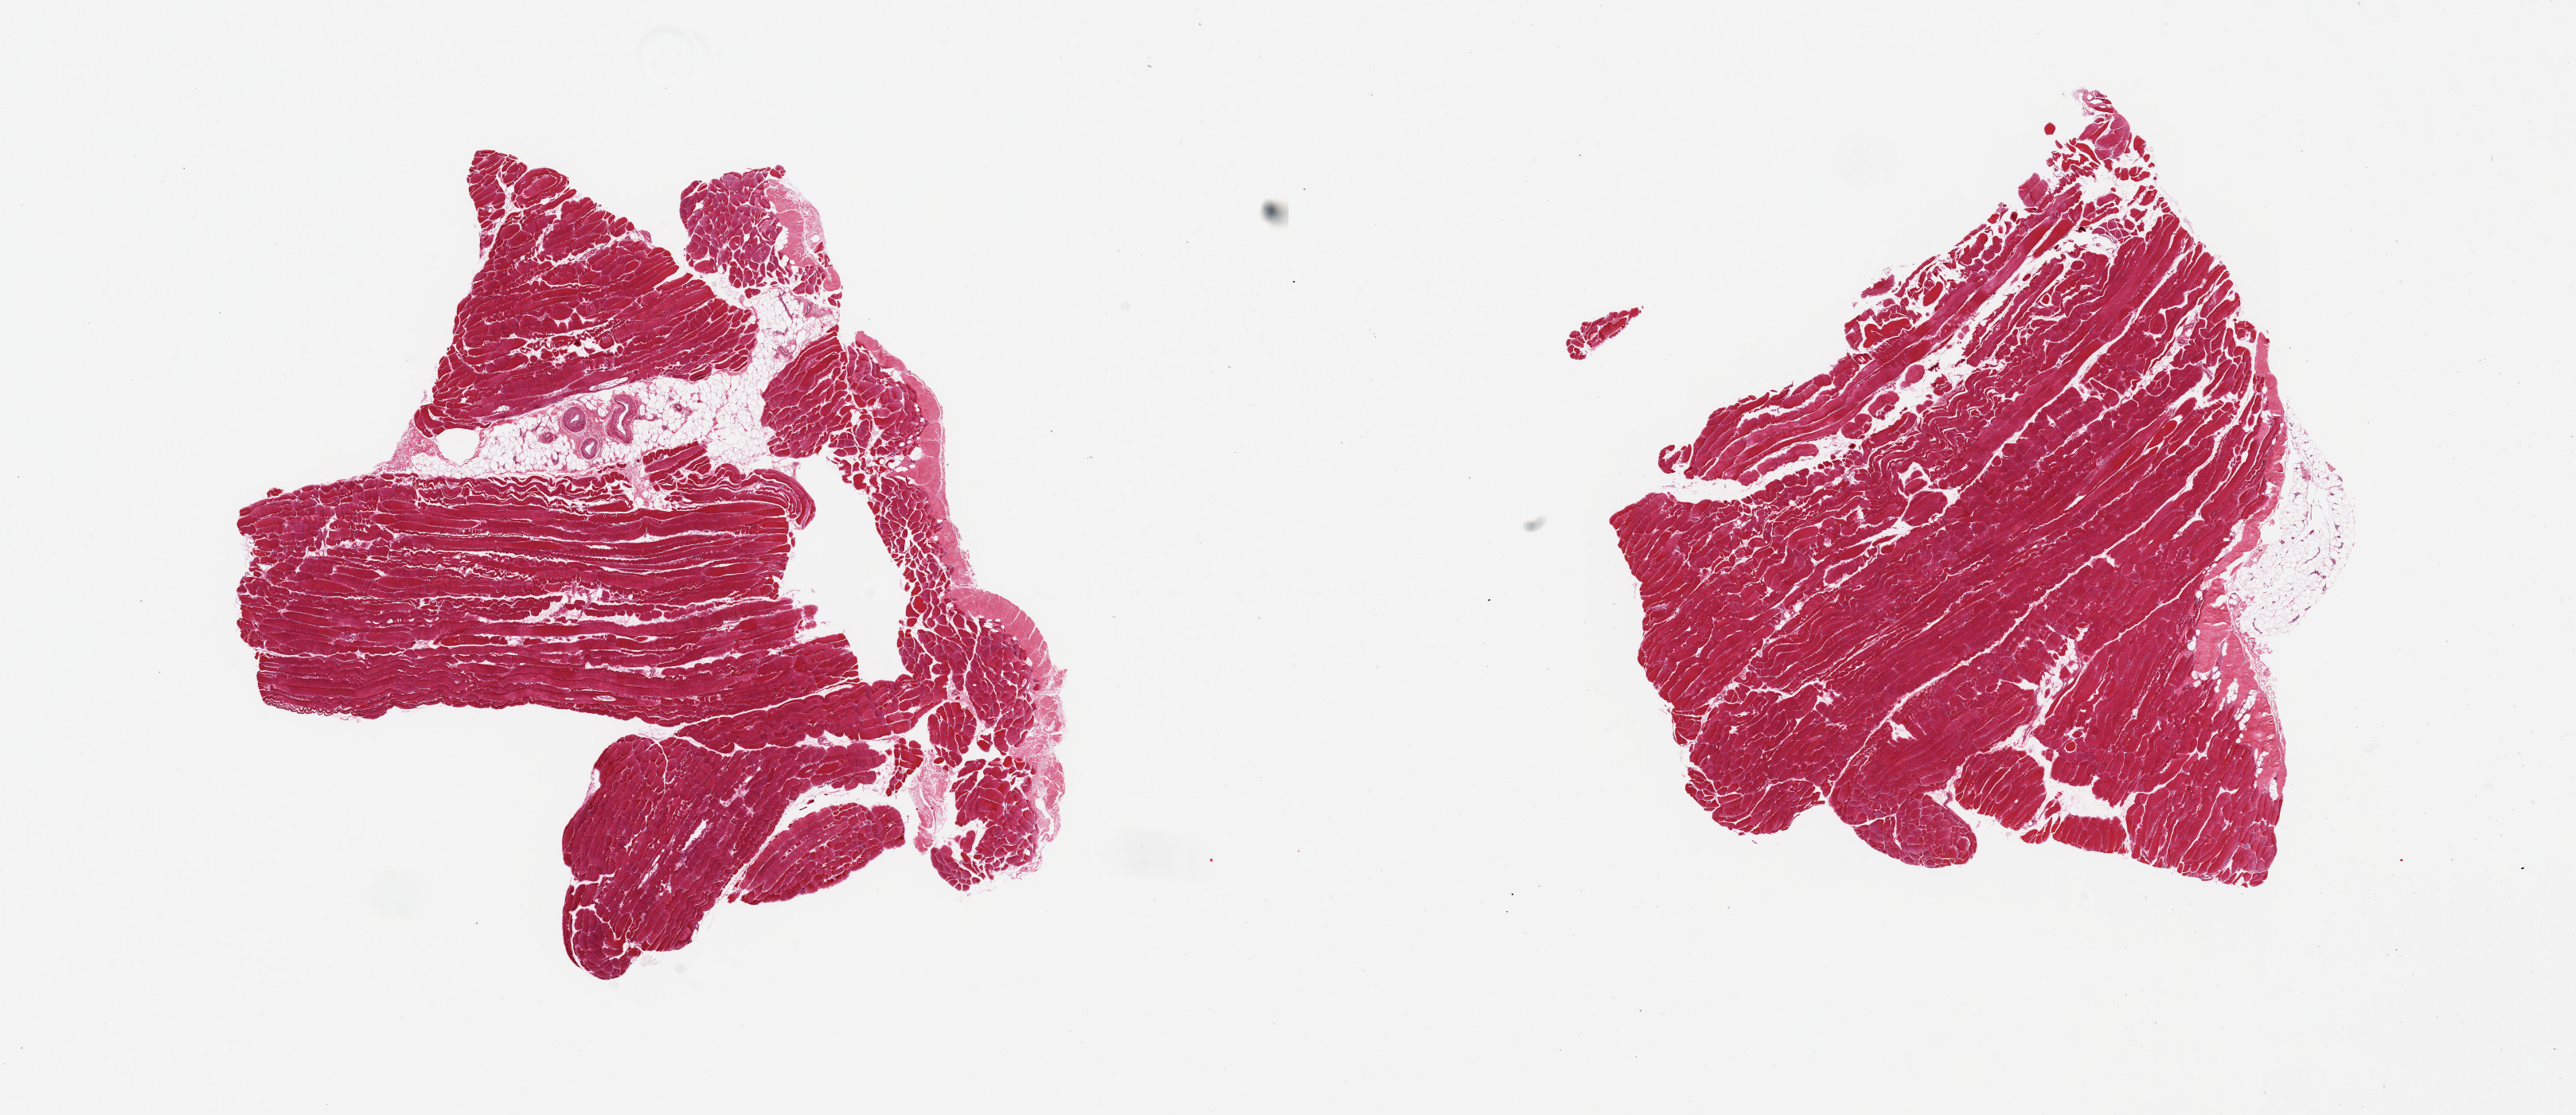
H&E whole-slide image, a low-resolution overview of the entire scanned area, about 25.6 x 11.1 mm, PAXgene-fixed paraffin-embedded (PFPE) section, section of skeletal muscle (target tissue), donor tissue sample. Donor sex: male.
- reviewer comment on this tissue sample: 2 pieces, some attached and internal adipose tissue and portion of tendon